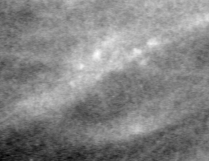
Region of interest cut from a scanned film mammogram (one marked finding), left breast, MLO view, BI-RADS breast density category 2 (scale 1–4).
- Calcifications, morphology pleomorphic, distribution clustered; BI-RADS assessment category 4; pathology result (as recorded, not read from the image): benign.